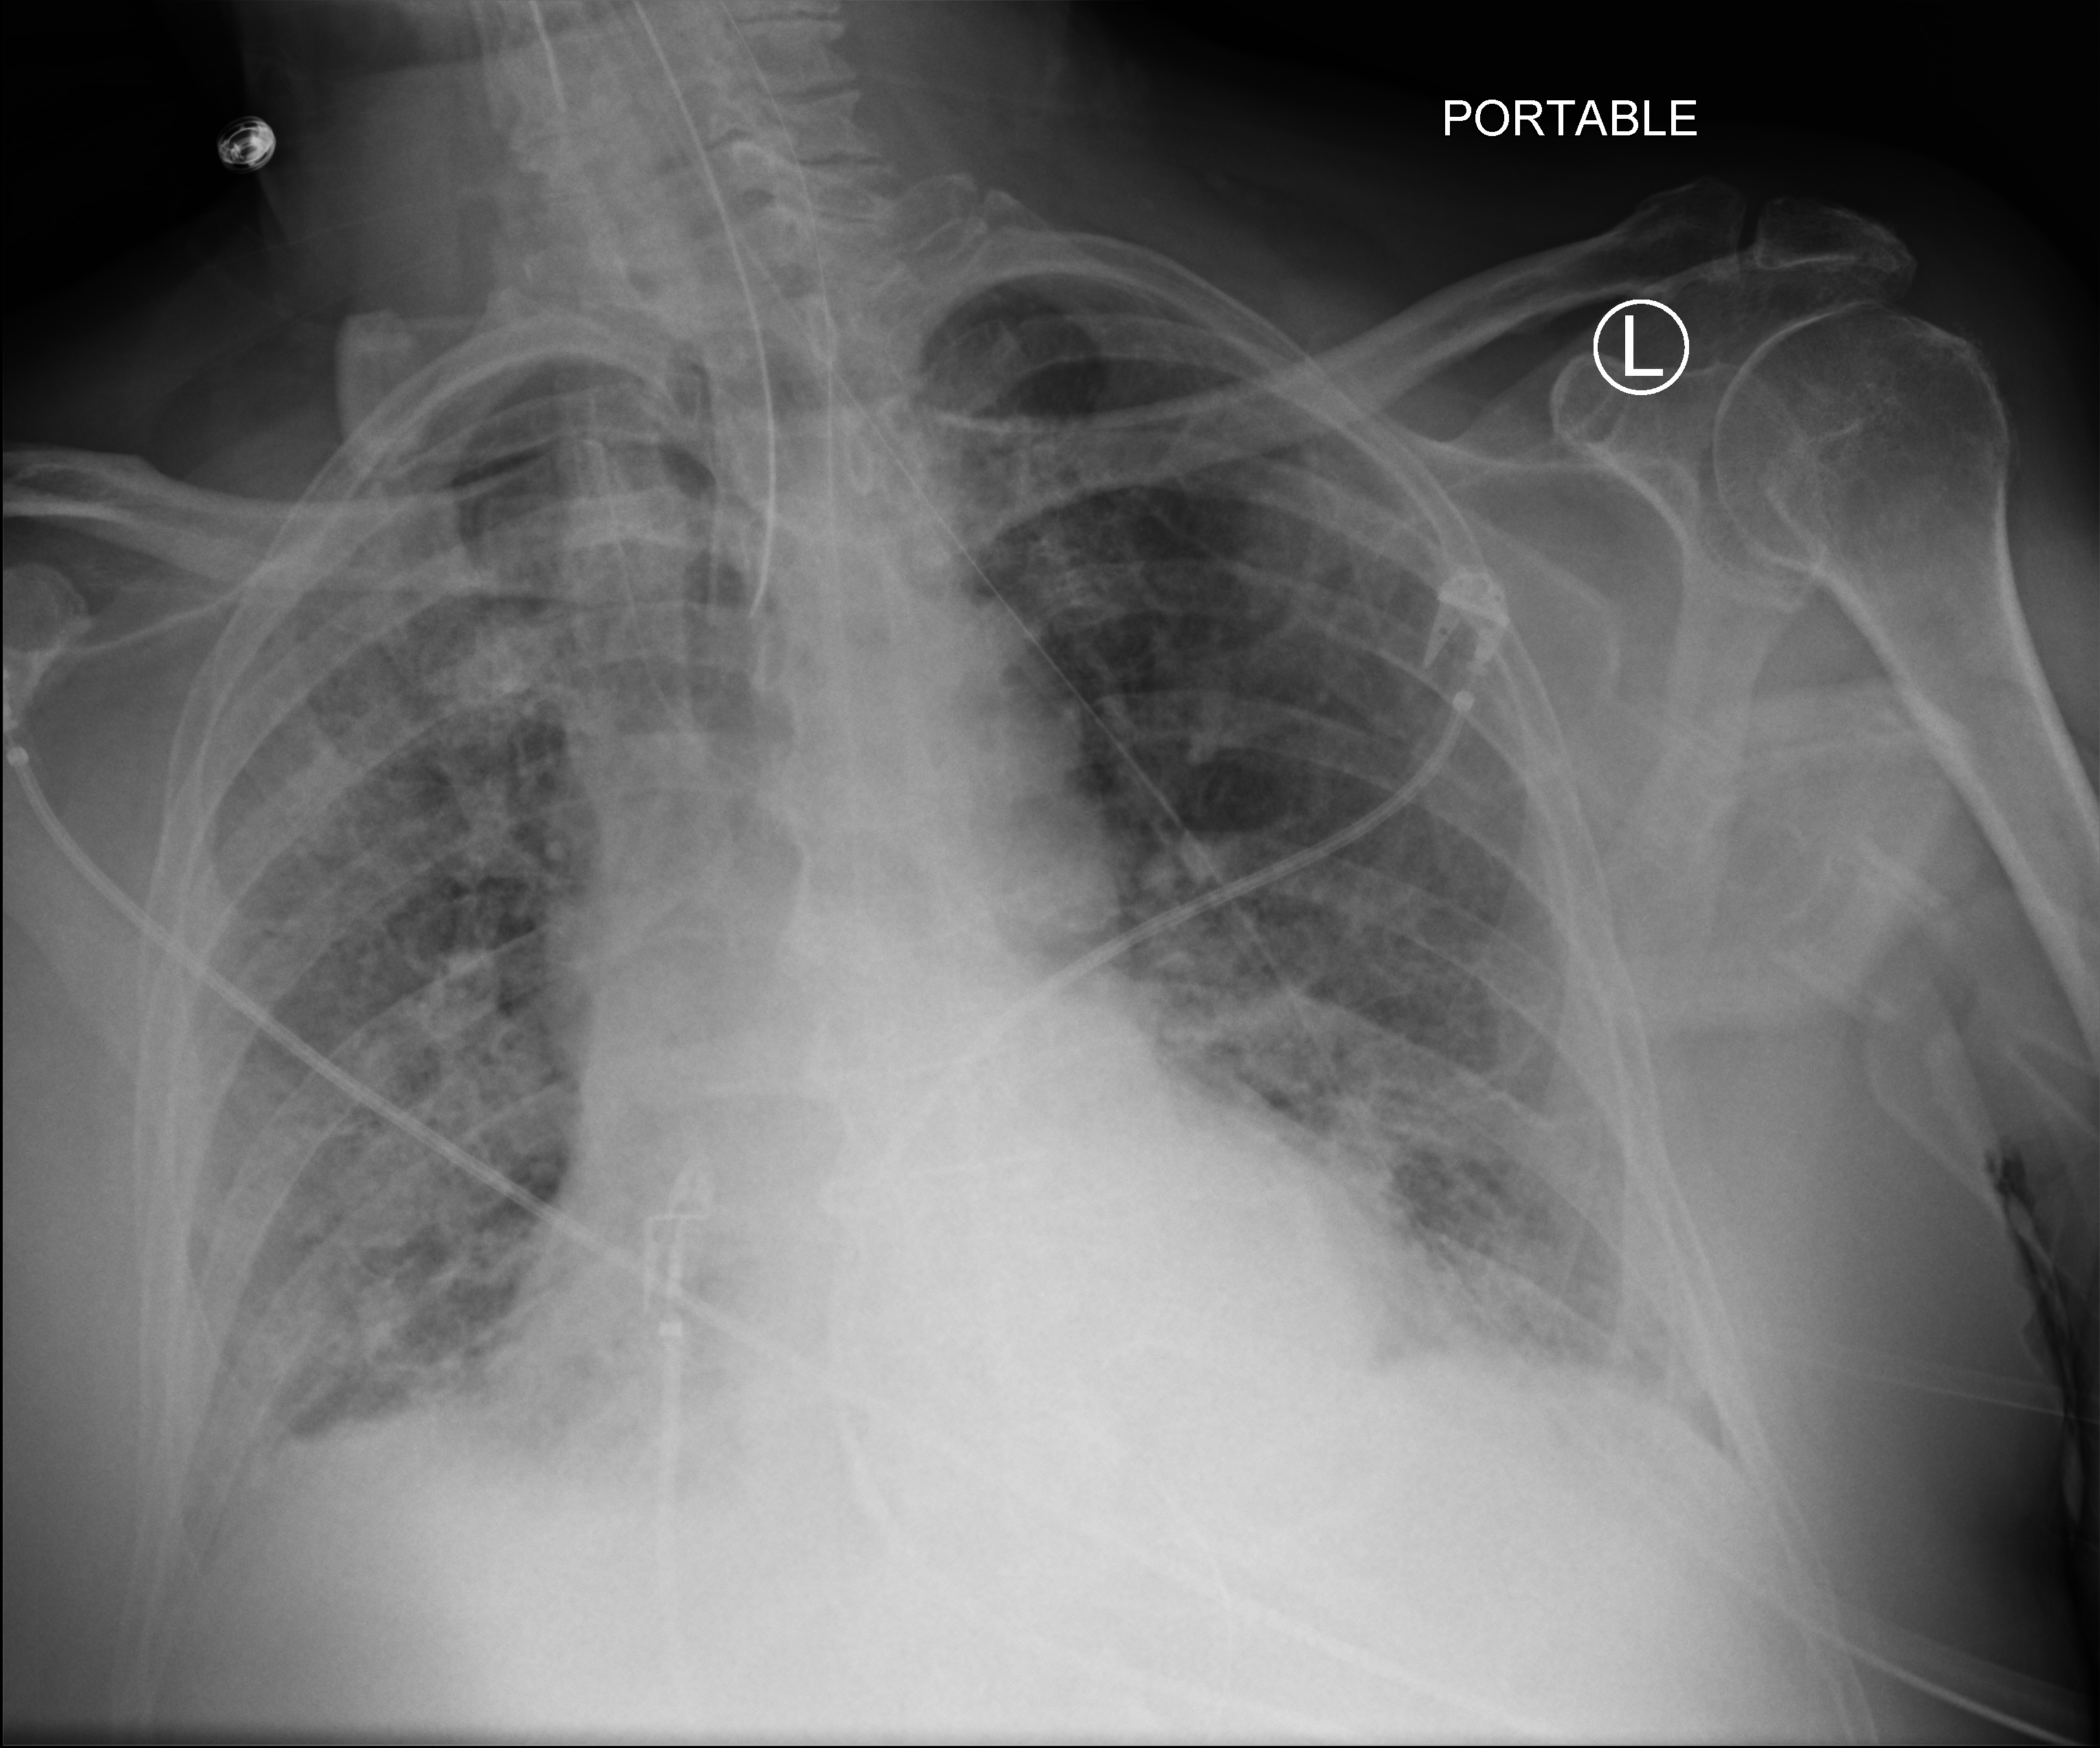
Portable chest radiograph, anteroposterior (AP) projection. Patient hospitalised with COVID-19; male, aged 75–90 years.
Admission-level facts for this patient (not findings on this image; timing relative to this image not recorded):
- mechanically ventilated during this hospital stay: yes
- smoking status (admission record): former
- hypertension (admission record): yes